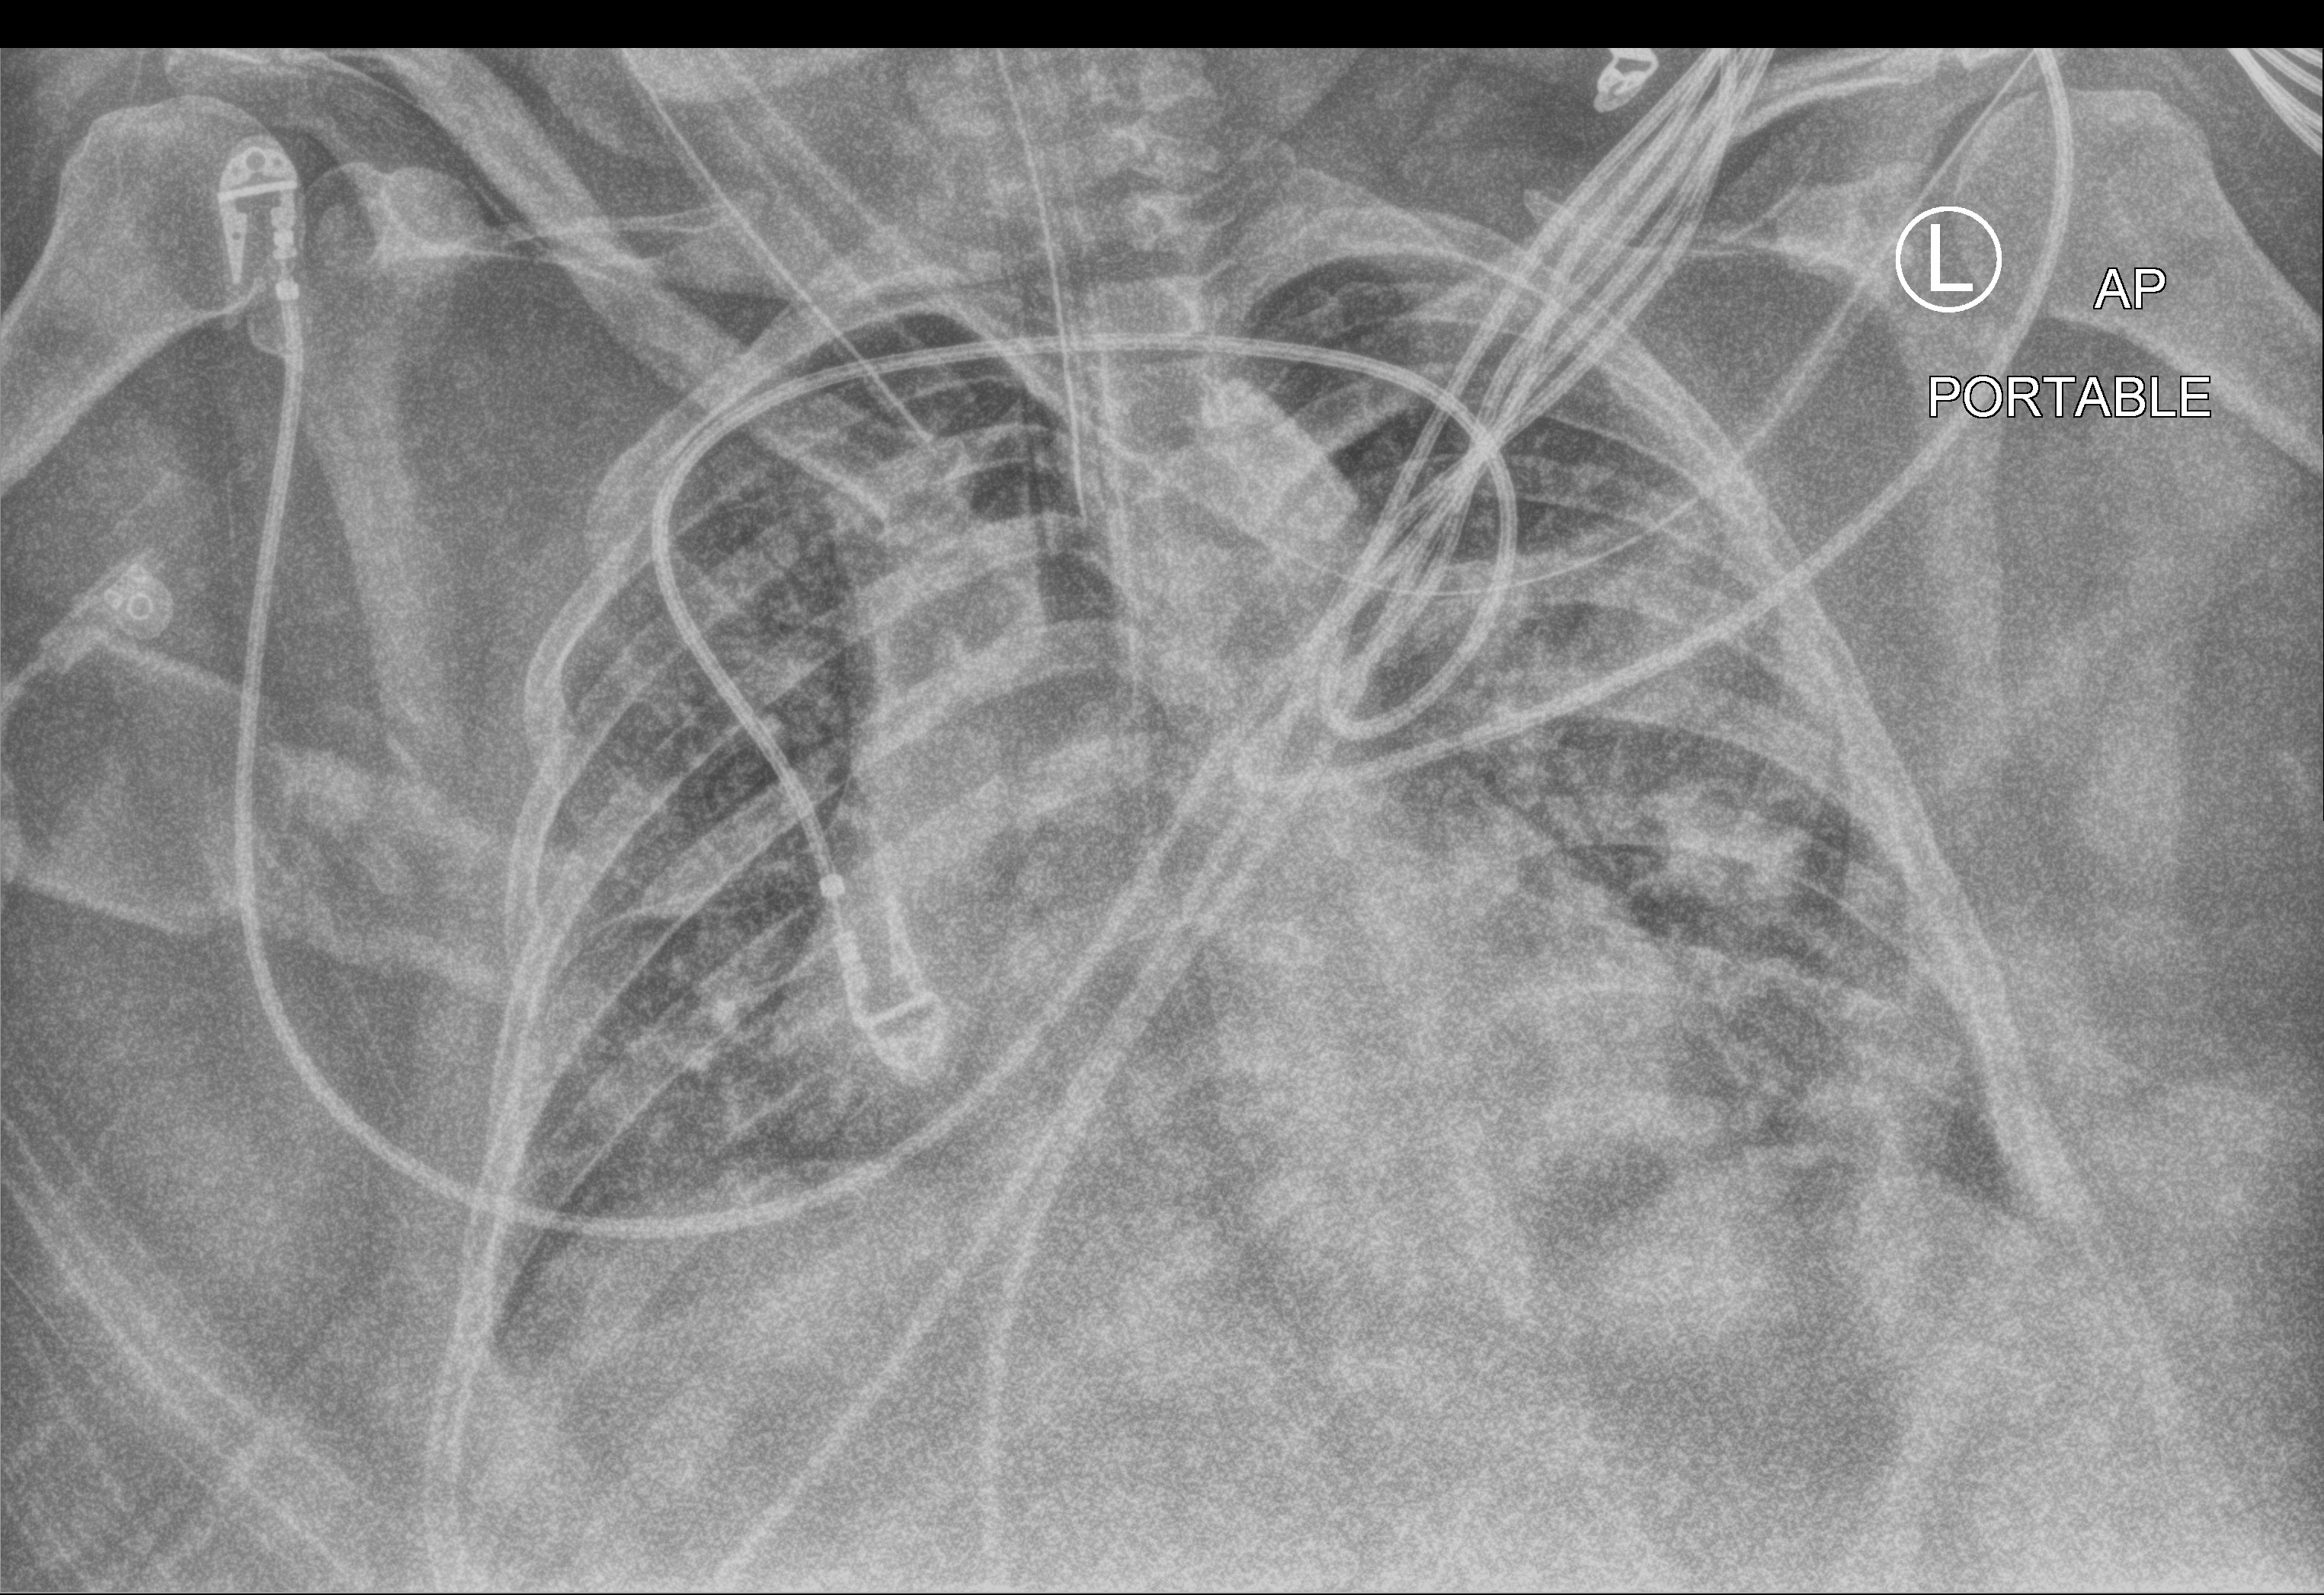
Bedside chest radiograph (computed radiography), anteroposterior (AP) projection. Female patient hospitalised with COVID-19, age 18–59 years.
Hospital-stay facts (about this admission, not read from this image; timing relative to this image not recorded): admitted to intensive care during this hospital stay: yes; hypertension (admission record): no.